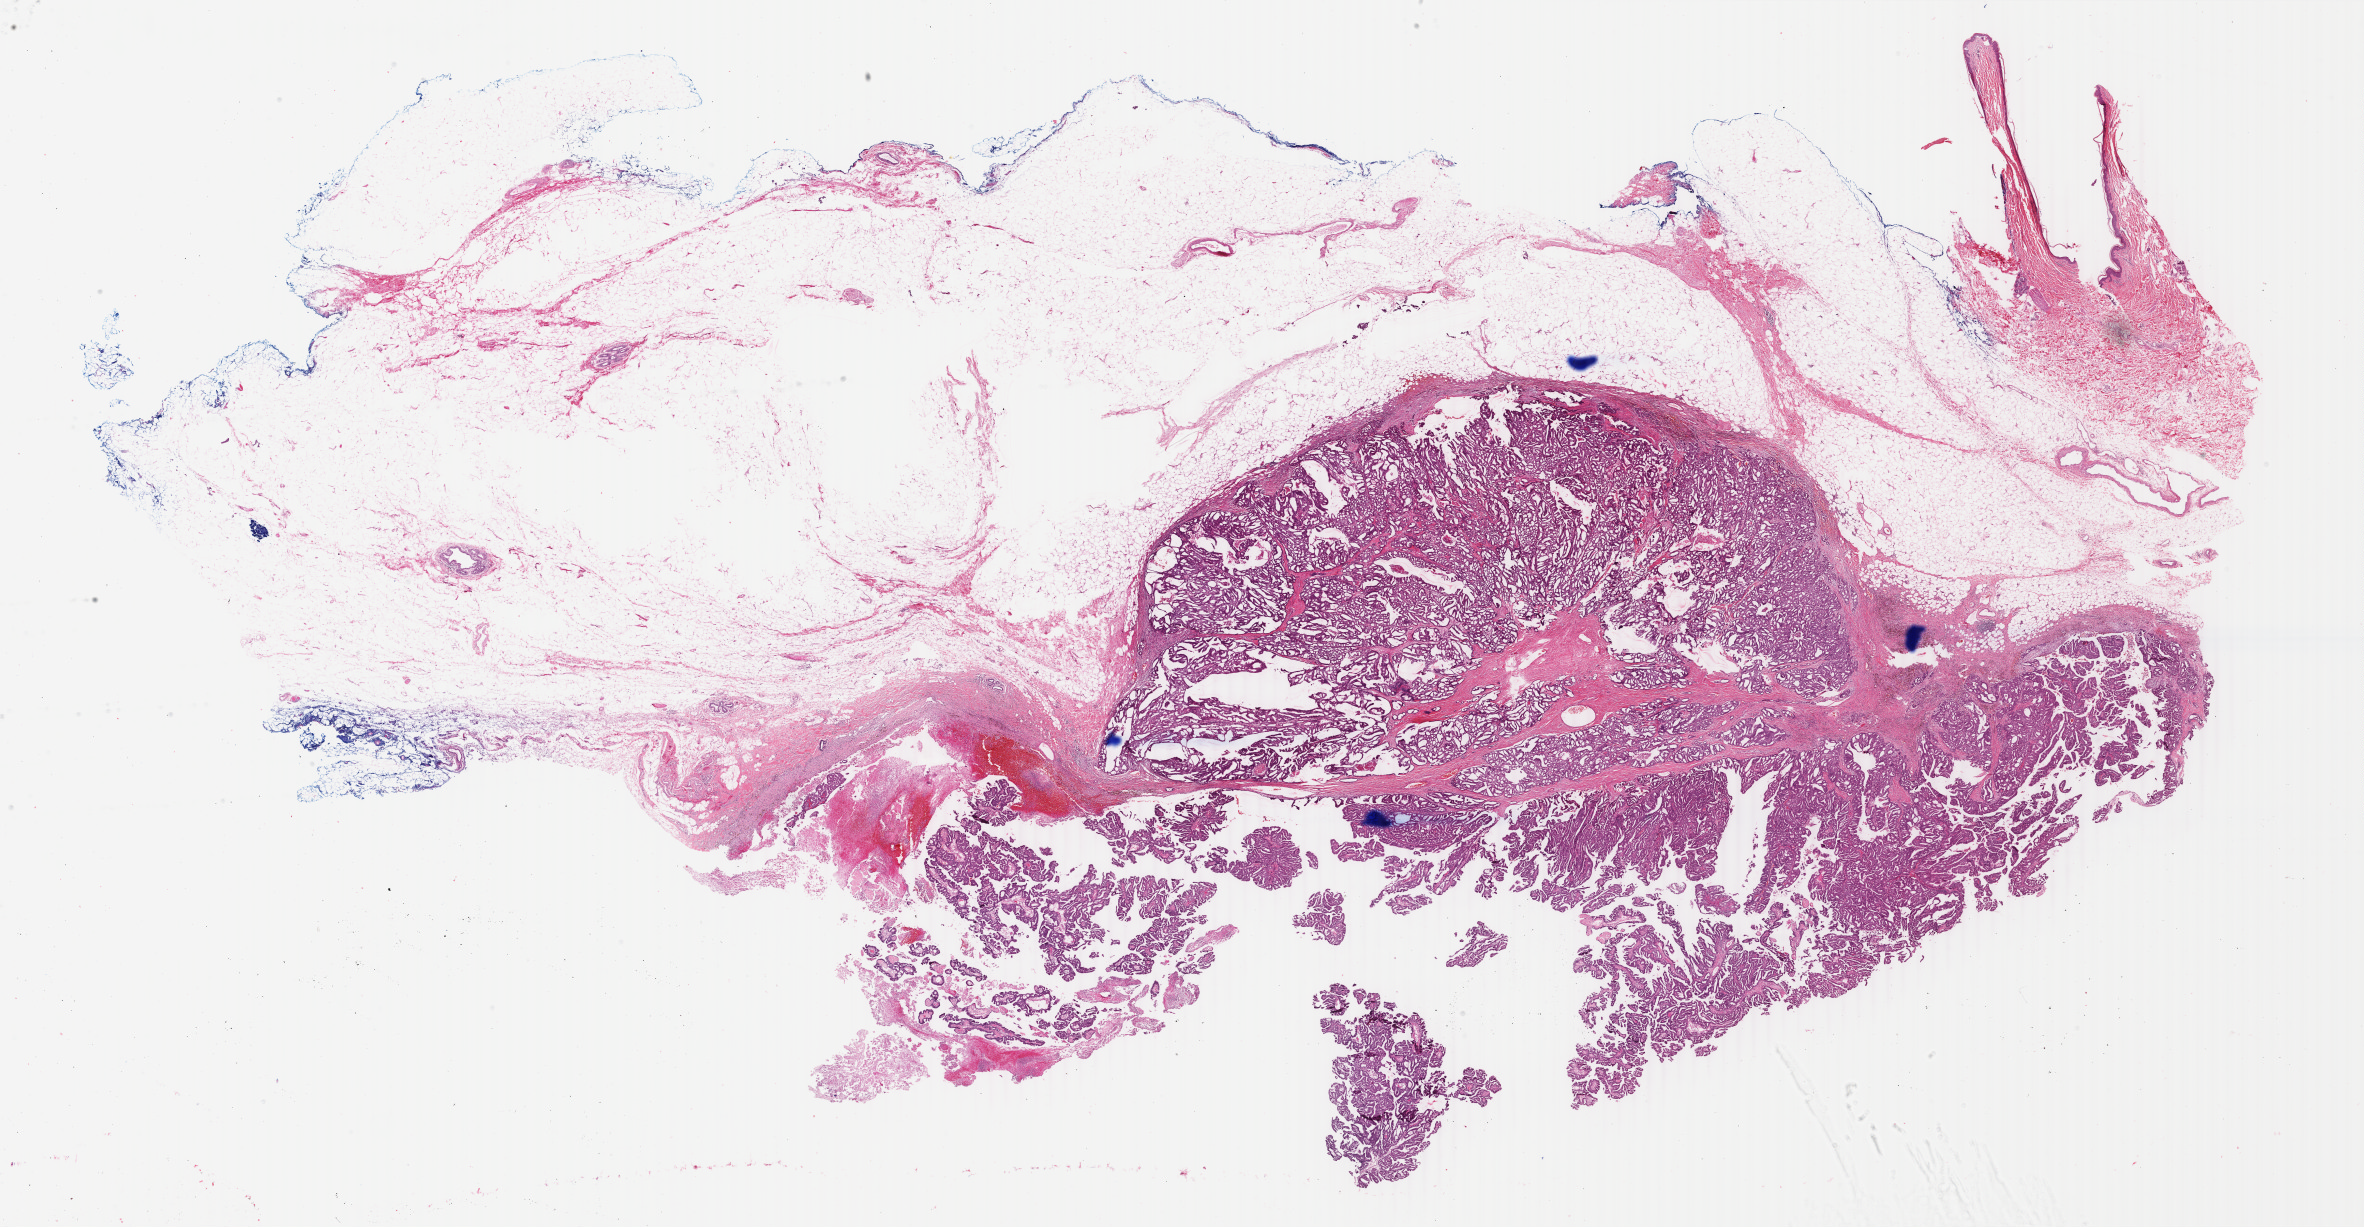
Whole-slide histology image, H&E, low-resolution overview of the scanned area, about 37.6 x 19.5 mm (slide scanned at 40x); formalin-fixed paraffin-embedded (FFPE) diagnostic section; primary tumour sample from the breast. Patient sex: female.
Histologic diagnosis: Intraductal papillary adenocarcinoma with invasion.